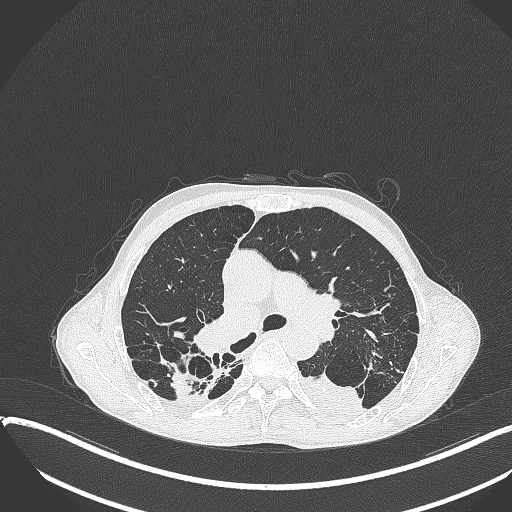
Chest CT, one axial slice. Position 245 of 401 along the scan axis. Reconstruction kernel B70f. 120 kVp. Lung window (W 1500 / L -600 HU). 512 × 512 image matrix. Male patient, age 57 years. From the clinical record (not read from this slice): clinical TNM (as recorded): T4 N0 M0.
Outlined on this slice (rectangle marked by the reading radiologist):
- lung tumour (recorded histology: squamous cell carcinoma): bounding box (x1, y1, x2, y2) in pixels: (298, 368, 367, 422)